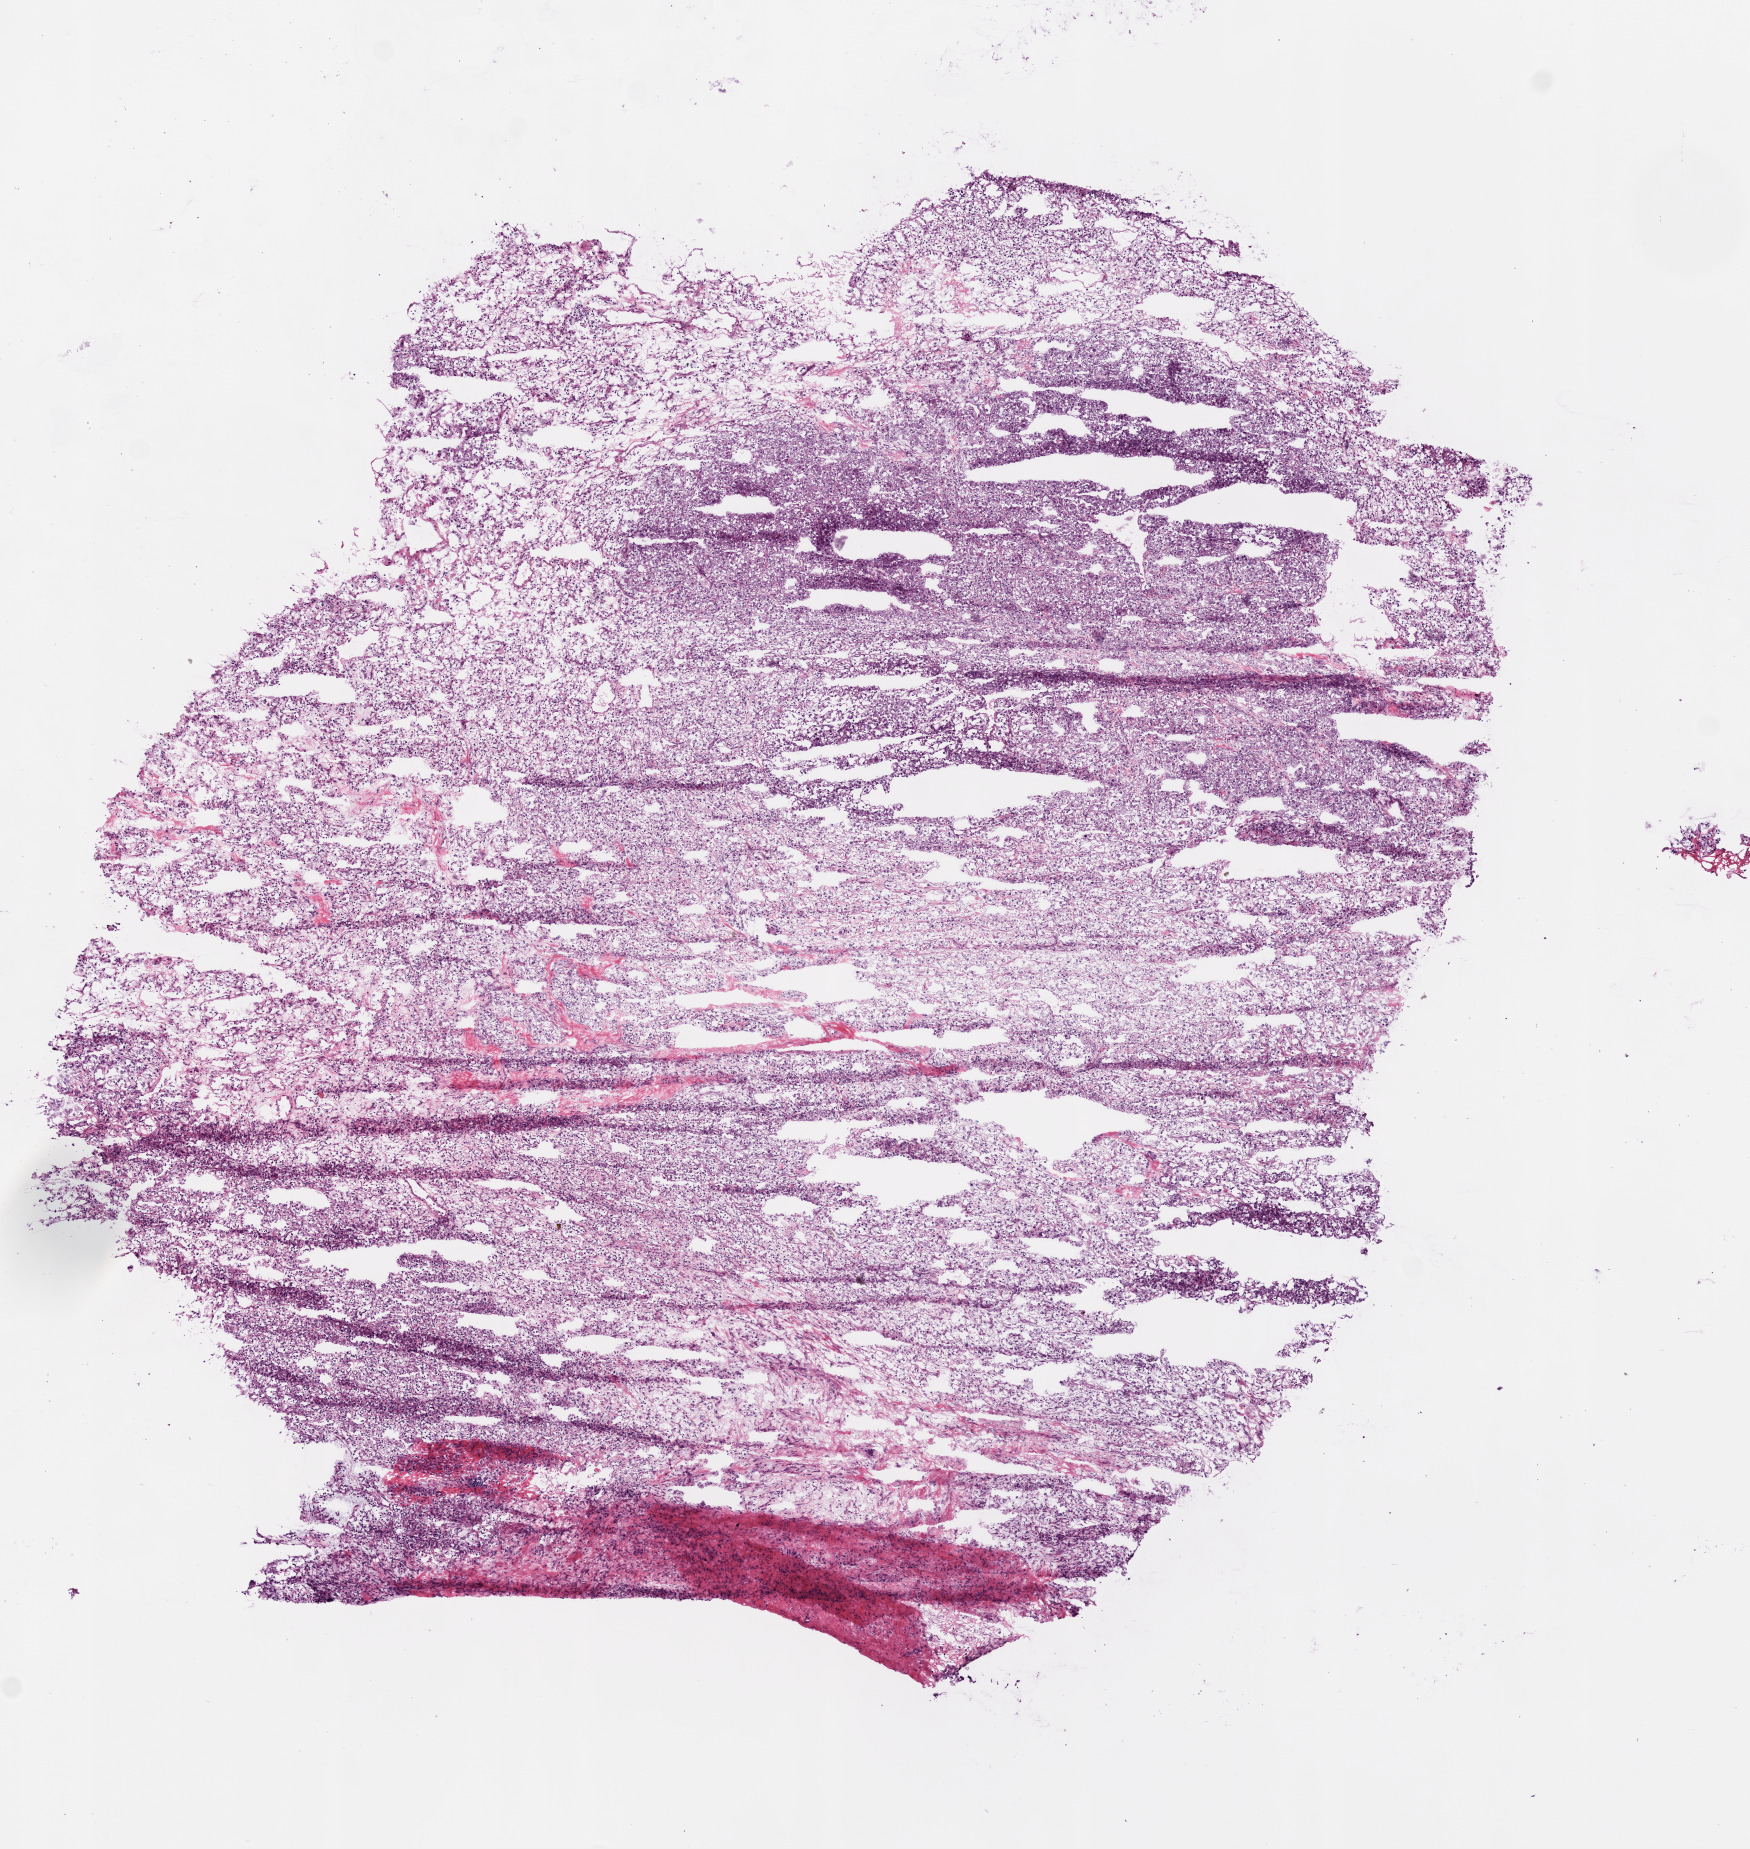
Hematoxylin and eosin (H&E) stained whole-slide image, whole scanned area (about 7.0 x 7.4 mm, acquisition: 20x scan) shown as a low-resolution overview. Frozen section from the bottom of the tissue portion. Primary tumour sample from the kidney. Male, age 49 years at initial diagnosis. Histologic grade: G2 (moderately differentiated). Pathologist review of this section (percent, as recorded): tumour cells 85%, tumour nuclei 65%, normal cells 5%, stromal cells 10%, necrosis 0%.
* laterality: left
* pathologic diagnosis: Clear cell adenocarcinoma, NOS
* AJCC pathologic stage: I